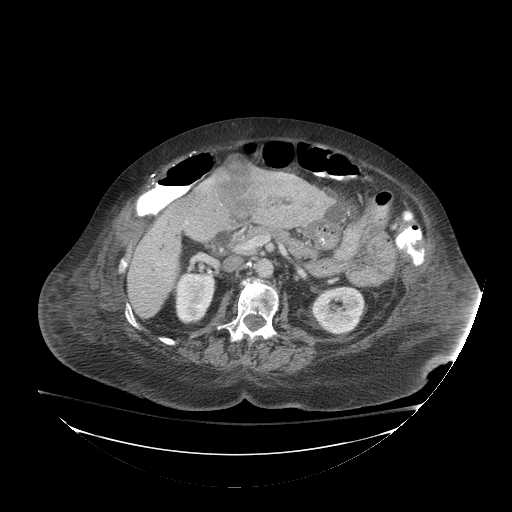
Contrast-enhanced abdominal CT (liver protocol), one axial slice; position 33 of 81 along the scan axis; soft-tissue window (W 400 / L 40 HU); 512 × 512 image matrix, field of view 500 × 500 mm. Case-level facts recorded for this patient, not image findings: diagnosis: hepatocellular carcinoma (patient treated with transarterial chemoembolisation; whether this scan precedes or follows treatment is not stated here); TNM stage (as recorded): Stage-I; Child-Pugh class: B; tumour differentiation: well-moderately differentiated; tumour nodularity: uninodular.
Annotated regions visible in this slice (semi-automatic segmentation, software-assisted and operator-edited):
- liver parenchyma outside the tumour (the mass and vessels are separate outlines, so this box may not span the whole liver): bounding box (x1, y1, x2, y2) in pixels: (122, 171, 312, 318)
- mass: (217, 155, 259, 214)
- liver vessels: (124, 263, 127, 267)